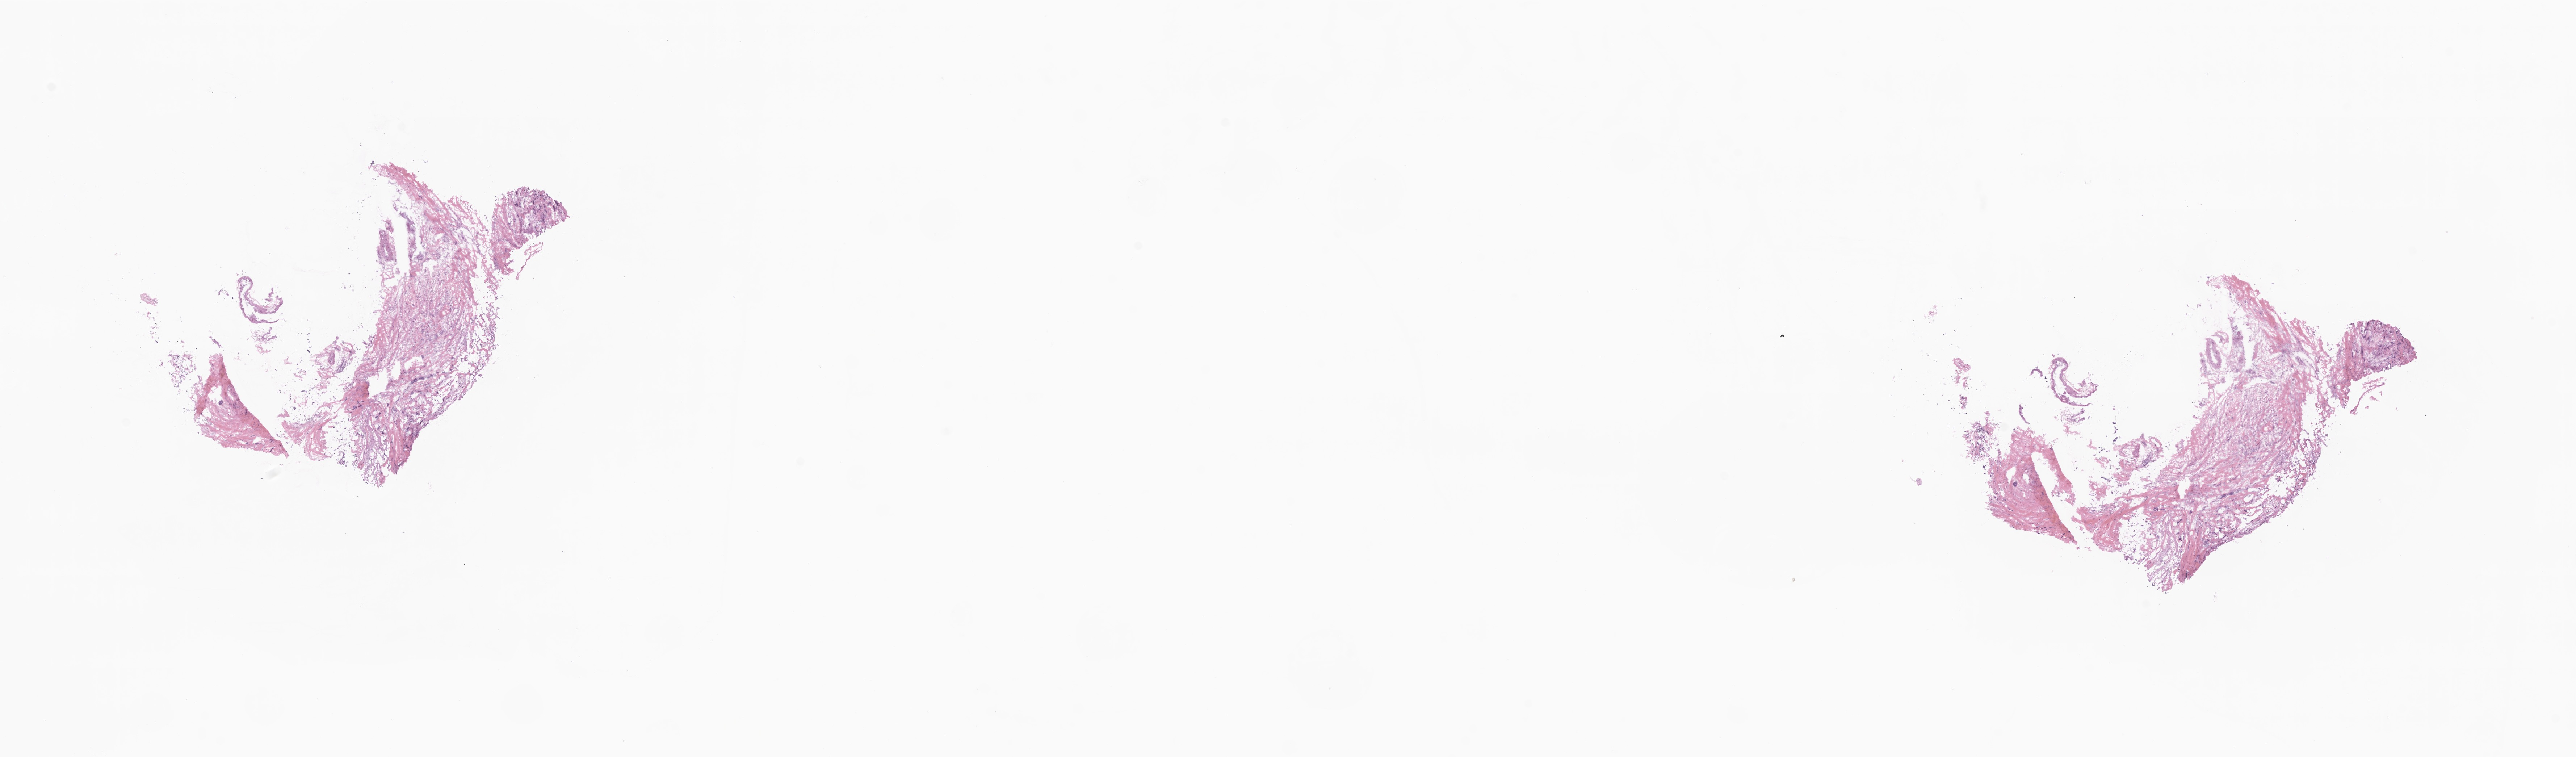
Haematoxylin and eosin whole-slide image, shown as a low-resolution overview of the whole scanned area (about 30.0 x 8.8 mm), frozen section, primary tumor, anatomic site: breast (left). Female, age 69 years at initial diagnosis. Pathologist review of this section (percent, as recorded): tumor cells 30%, tumor nuclei 50%, stromal cells 70%, necrosis 0%, normal cells 0%. Inflammatory infiltration, as recorded: lymphocyte infiltration 0%, monocyte infiltration 0%, neutrophil infiltration 0%.
Histologic diagnosis: Infiltrating duct carcinoma, NOS.